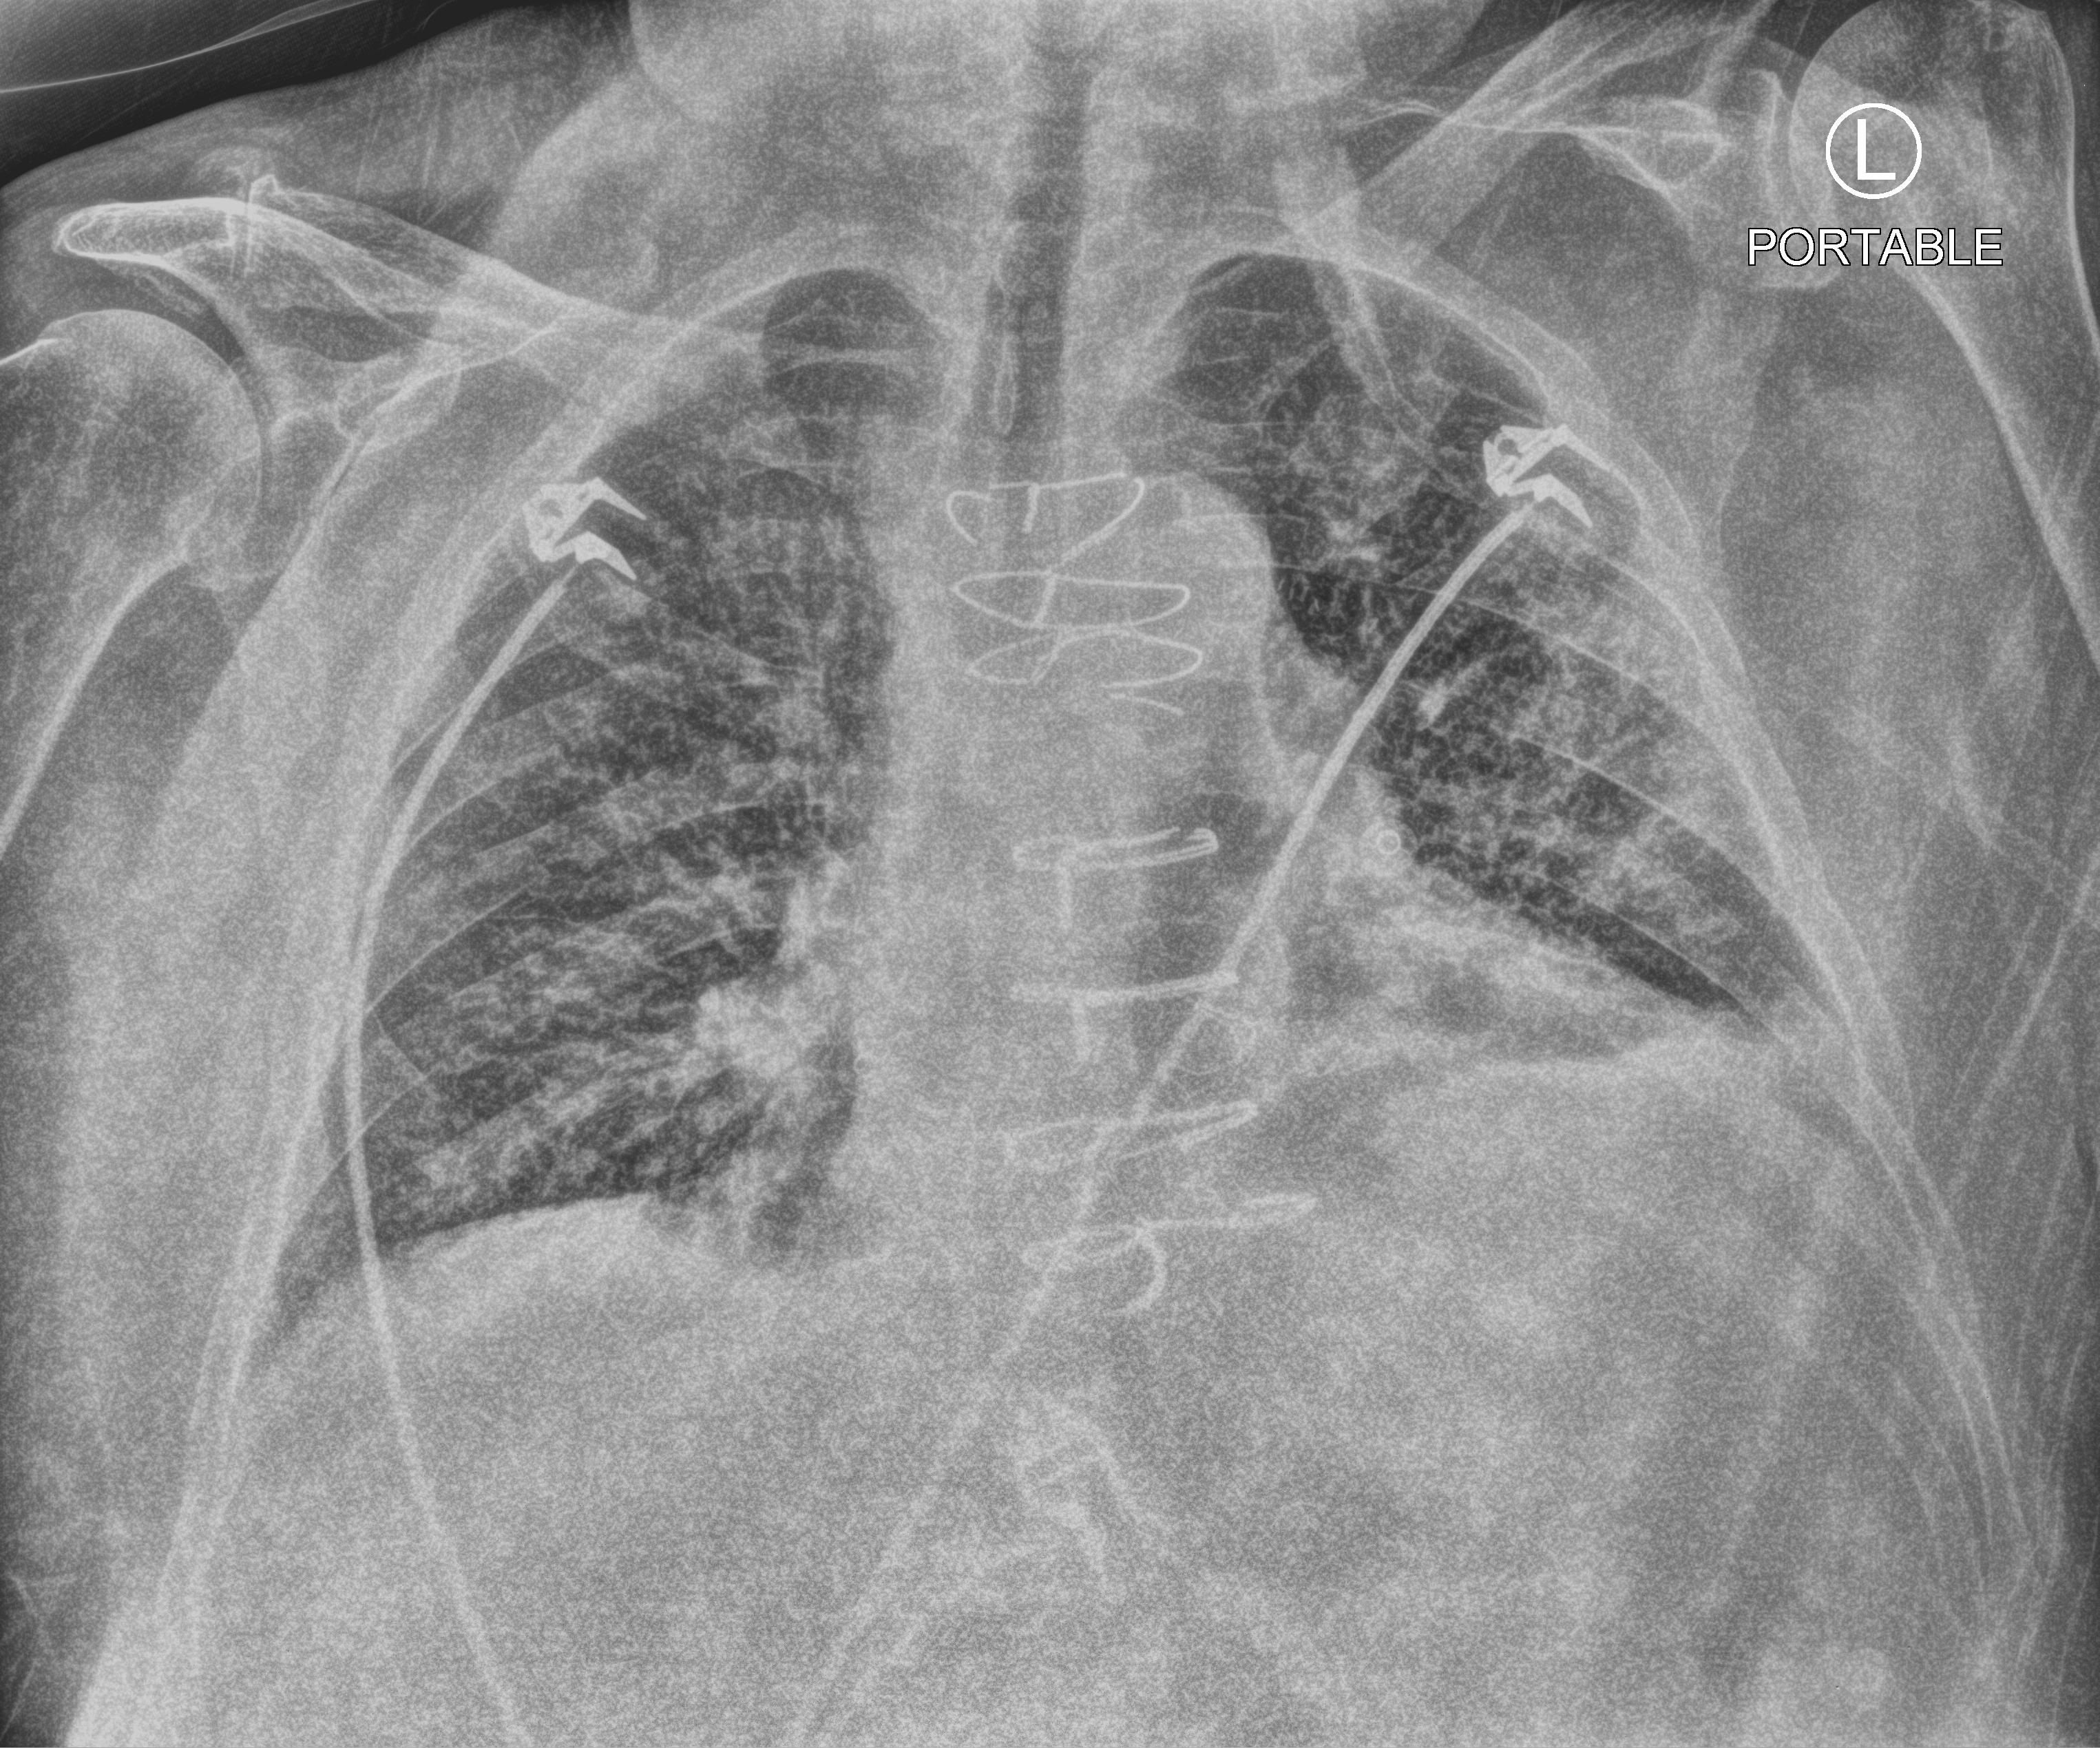
Portable chest radiograph; anteroposterior (AP) projection. Male patient hospitalised with COVID-19, age 75–90 years.
Hospital-stay facts (about this admission, not read from this image; timing relative to this image not recorded): mechanically ventilated during this hospital stay: no; admitted to intensive care during this hospital stay: no.